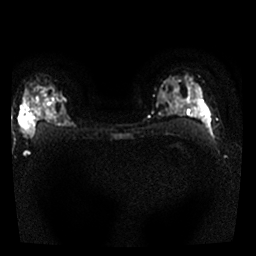
Breast MRI, one axial slice; diffusion-weighted series; image 2 of 4 stored at this slice position (different b-values; order by instance number); 1.5 T; 4 mm slice thickness; 256 × 256 image matrix. Female patient.
Annotated regions visible in this slice (outlined manually by an expert reader):
- tumour on diffusion-weighted imaging: box from (x=21, y=104) to (x=35, y=136) px